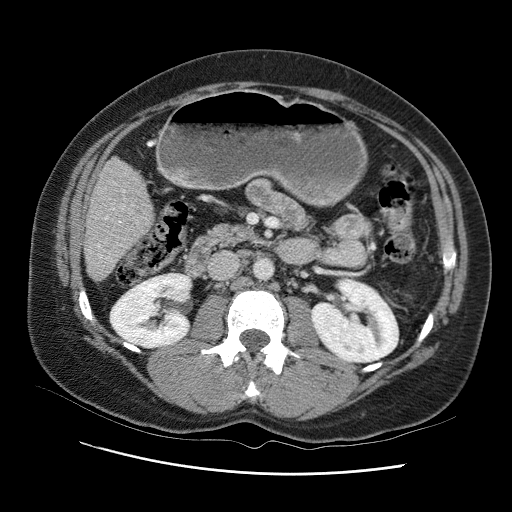
Contrast-enhanced abdominal CT (liver protocol), one axial slice; position 30 of 95 along the scan axis; one of 2 acquisitions stored at this slice position; soft-tissue window (W 400 / L 40 HU); 2.5 mm slice thickness; 512 × 512 image matrix, field of view 360 × 360 mm. Case-level facts recorded for this patient, not image findings: diagnosis: hepatocellular carcinoma (patient treated with transarterial chemoembolisation; whether this scan precedes or follows treatment is not stated here); TNM stage (as recorded): Stage-I; Child-Pugh class: B.
Outlined on this slice (semi-automatically segmented with operator editing):
- liver parenchyma outside the tumour (the mass and vessels are separate outlines, so this box may not span the whole liver): box from (x=84, y=144) to (x=162, y=286) px
- liver vessels: (x=101, y=164)–(x=135, y=251)